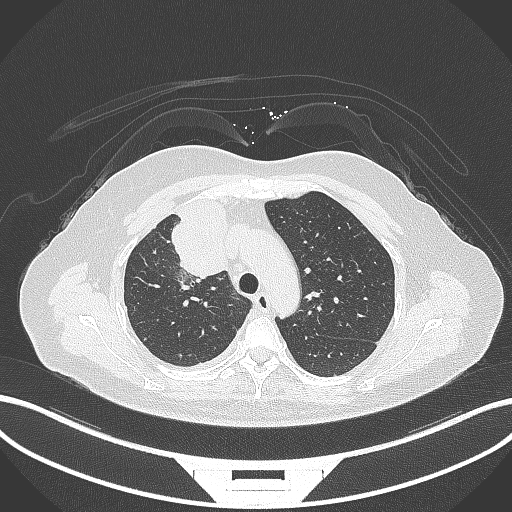
Chest CT, one axial slice; slice 216 of 305 in the series (ordered by position); reconstruction kernel B70f; 120 kVp; lung window (W 1500 / L -600 HU); 1 mm slice thickness; 512 × 512 image matrix. Patient: female, 52 years. Case-level facts recorded for this patient, not image findings: clinical TNM (as recorded): T3 N1 M1.
Structures marked on this image (bounding box drawn by a radiologist):
- lung tumour (recorded histology: adenocarcinoma): box from (x=169, y=196) to (x=233, y=280) px